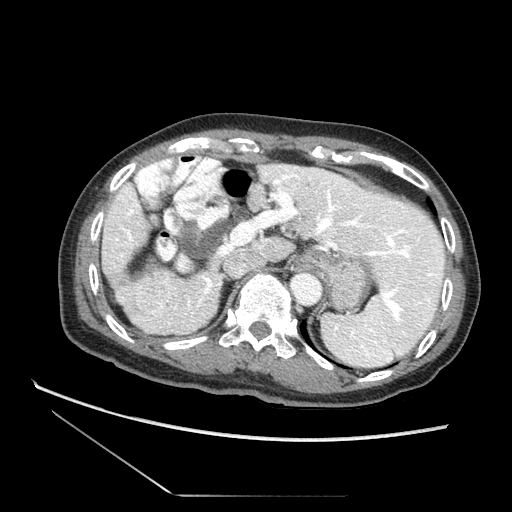
Contrast-enhanced abdominal CT (liver protocol), one axial slice; slice 54 of 73 in the series (ordered by position); 120 kVp; soft-tissue window (W 400 / L 40 HU); 2.5 mm slice thickness; 512 × 512 image matrix, field of view 360 × 360 mm. From the clinical record (not read from this slice): diagnosis: hepatocellular carcinoma (patient treated with transarterial chemoembolisation; whether this scan precedes or follows treatment is not stated here); TNM stage (as recorded): Stage-II; Child-Pugh class: A; tumour differentiation: moderately differentiated; tumour nodularity: multinodular.
Annotated regions visible in this slice (semi-automatically segmented with operator editing):
- liver parenchyma outside the tumour (the mass and vessels are separate outlines, so this box may not span the whole liver): box from (x=103, y=164) to (x=447, y=355) px
- mass: (x=142, y=277)–(x=171, y=307)
- liver vessels: (x=159, y=231)–(x=395, y=308)